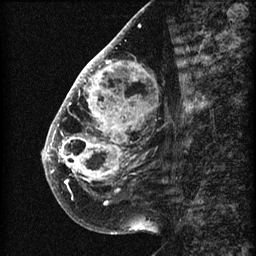
Breast MRI (dynamic contrast-enhanced), one sagittal slice. Slice 25 of 60 in the series (ordered by position). 3 images stored at this slice position (order not interpretable as contrast timing). 1.5 T. TE 4.2 ms, TR 22.7 ms. 256 × 256 image matrix, field of view 180 × 180 mm. Female patient, age 48 years. From the clinical record (not read from this slice): setting: breast cancer imaged before/during neoadjuvant chemotherapy; receptor status: triple-negative.
Annotated regions visible in this slice (semi-automatically segmented with operator editing):
- analysis volume of interest (the breast-tissue region the enhancement analysis was run in; not a lesion): box from (x=44, y=30) to (x=173, y=207) px
- tumour enhancement mask (voxels above the 90 % enhancement threshold inside the analysis volume of interest): (x=44, y=39)–(x=137, y=191)